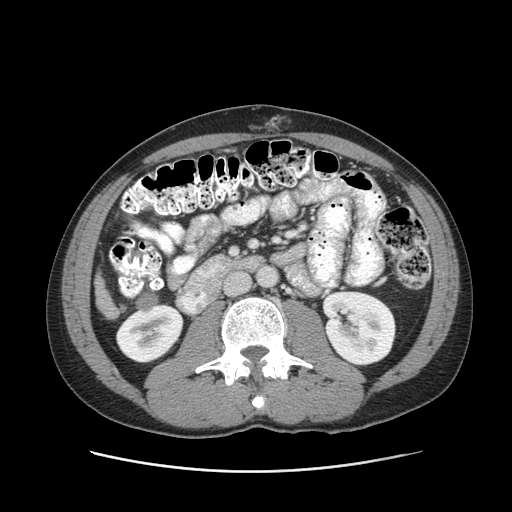
Contrast-enhanced abdominal CT (liver protocol), one axial slice. Position 24 of 93 along the scan axis. Reconstruction kernel STANDARD. Soft-tissue window (W 400 / L 40 HU). 2.5 mm slice thickness. 512 × 512 image matrix, field of view 380 × 380 mm. From the clinical record (not read from this slice): diagnosis: hepatocellular carcinoma (patient treated with transarterial chemoembolisation; whether this scan precedes or follows treatment is not stated here); TNM stage (as recorded): Stage-II; Child-Pugh class: A; tumour differentiation: moderately differentiated; tumour size: 1 cm.
Structures marked on this image (semi-automatically segmented with operator editing):
- liver parenchyma outside the tumour (the mass and vessels are separate outlines, so this box may not span the whole liver): bounding box [x1, y1, x2, y2] px = [94, 273, 114, 318]